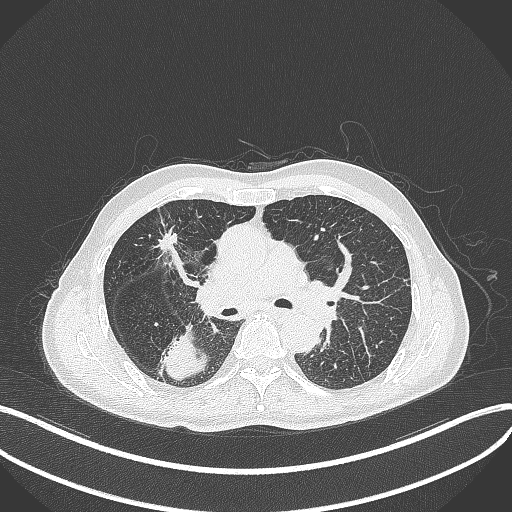
Chest CT, one axial slice; position 272 of 428 along the scan axis; reconstruction kernel B70f; 120 kVp; lung window (W 1500 / L -600 HU); 512 × 512 image matrix, field of view 400 × 400 mm. Male patient, age 79 years. Case-level facts recorded for this patient, not image findings: clinical TNM (as recorded): T3 N0 M0.
Outlined on this slice (bounding box drawn by a radiologist):
- lung tumour (recorded histology: adenocarcinoma): bounding box <159,323,212,383> (left, top, right, bottom; pixels)